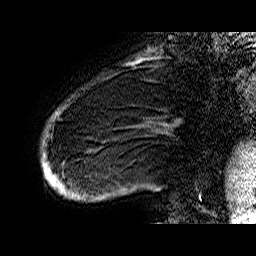
Breast MRI (dynamic contrast-enhanced), one sagittal slice. Position 8 of 60 along the scan axis. Dynamic contrast-enhanced series, time point 2 of 6 at this slice position (early post-contrast). 1.5 T. TE 6.4 ms, TR 32.9 ms. 4 mm slice thickness. 256 × 256 image matrix. Female patient. From the clinical record (not read from this slice): setting: breast cancer imaged before/during neoadjuvant chemotherapy; receptor status: HR-positive, HER2-negative.
Annotated regions visible in this slice (semi-automatic segmentation, software-assisted and operator-edited):
- analysis volume of interest (the breast-tissue region the enhancement analysis was run in; not a lesion): bounding box <42,87,168,207> (left, top, right, bottom; pixels)
- tumour enhancement mask (voxels above the 100 % enhancement threshold inside the analysis volume of interest): <42,154,67,197>